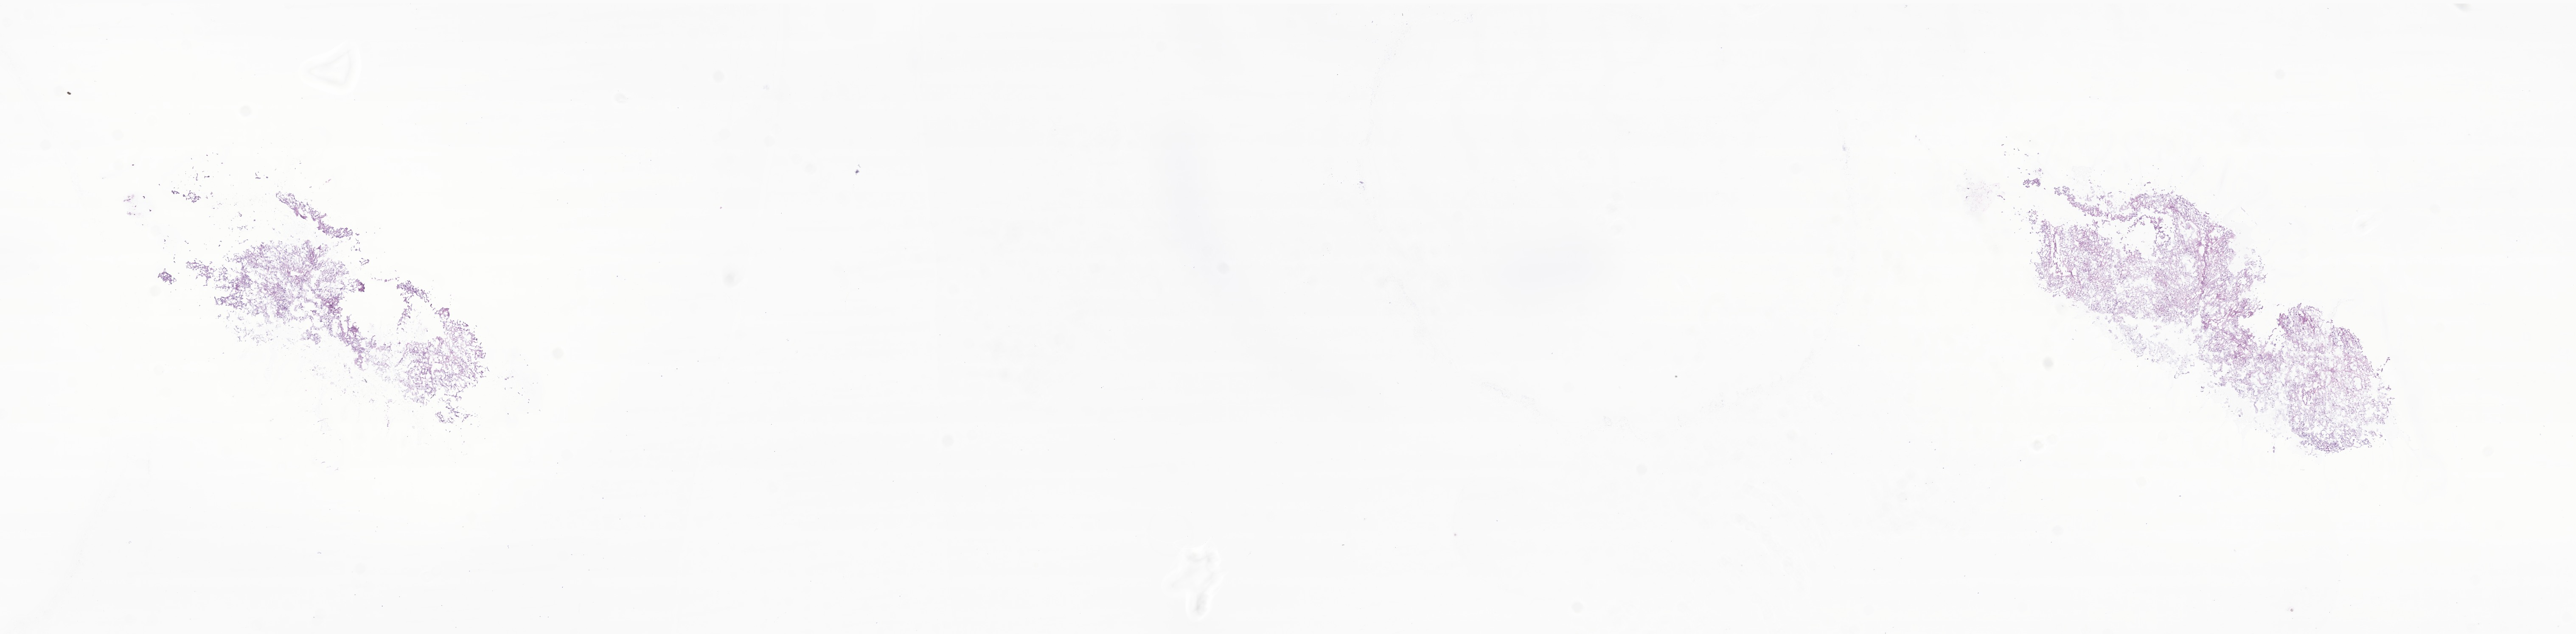
Digitized haematoxylin and eosin-stained section of tumor tissue from the cerebellum, low-resolution overview of the scanned area, about 25.6 x 6.3 mm; frozen section (OCT-embedded). Patient: male, age 101 months (8 years 5 months).
Recorded diagnosis: Pilocytic astrocytoma.